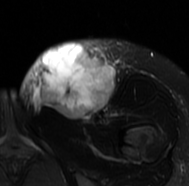
MRI of an extremity soft-tissue mass, one axial slice. T2-weighted fat-saturated. MR volume resampled by the dataset authors to the PET/CT grid (not the native acquisition matrix). 3.27 mm slice thickness. 189 × 186 image matrix. Female patient. Case-level facts recorded for this patient, not image findings: histological type: leiomyosarcoma; grade: high; site of the primary tumour: groin.
Structures marked on this image (expert contour drawn on MRI and transferred to this co-registered scan by the dataset authors):
- gross tumour volume including surrounding oedema: bounding box [x1, y1, x2, y2] px = [19, 38, 134, 121]
- gross tumour volume (mass): [33, 43, 114, 119]